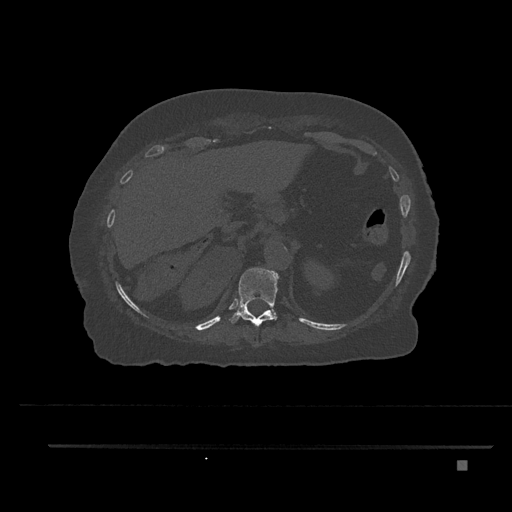
CT including the spine, one axial slice; position 311 of 797 along the scan axis; reconstruction kernel Br40s/3; 120 kVp; bone window (W 1800 / L 400 HU); 0.5 mm slice thickness; 512 × 512 image matrix. Female patient, age 76 years. From the clinical record (not read from this slice): primary cancer: lung; vertebrae with lytic lesions (as recorded): T11, L3.
Outlined on this slice (semi-automatically segmented with operator editing):
- T10 vertebra: bounding box (x1, y1, x2, y2) in pixels: (256, 344, 258, 346)
- T11 vertebra: (229, 268, 279, 326)